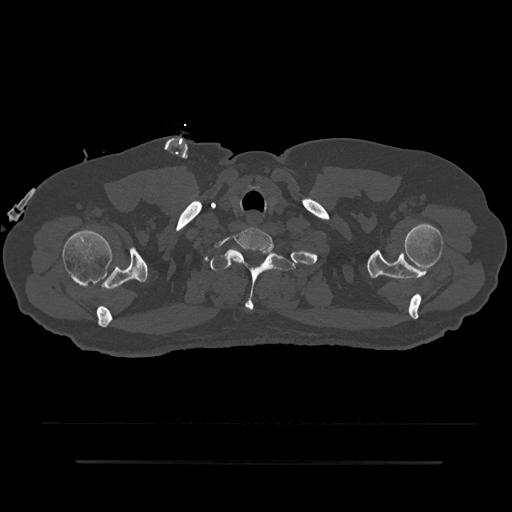
CT including the spine, one axial slice. Slice 751 of 797 in the series (ordered by position). Reconstruction kernel Br40s/3. 120 kVp. Bone window (W 1800 / L 400 HU). 512 × 512 image matrix, field of view 464 × 464 mm. Male patient, age 59 years. From the clinical record (not read from this slice): primary cancer: bile ducts.
Annotated regions visible in this slice (semi-automatically segmented with operator editing):
- T1 vertebra: bounding box (x1, y1, x2, y2) in pixels: (210, 249, 295, 311)